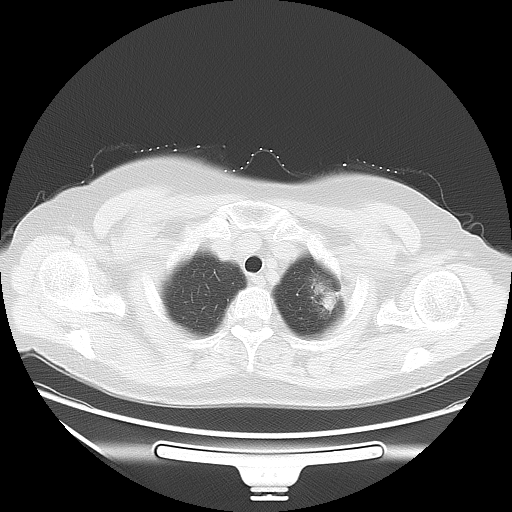
Chest CT, one axial slice; position 49 of 53 along the scan axis; reconstruction kernel LUNG; 120 kVp; lung window (W 1500 / L -600 HU); 512 × 512 image matrix, field of view 403 × 403 mm. Female patient, age 66 years. From the clinical record (not read from this slice): clinical TNM (as recorded): T2 N0 M0; histopathological grade: G2.
Annotated regions visible in this slice (rectangle marked by the reading radiologist):
- lung tumour (recorded histology: adenocarcinoma): bounding box (x1, y1, x2, y2) in pixels: (301, 257, 340, 328)